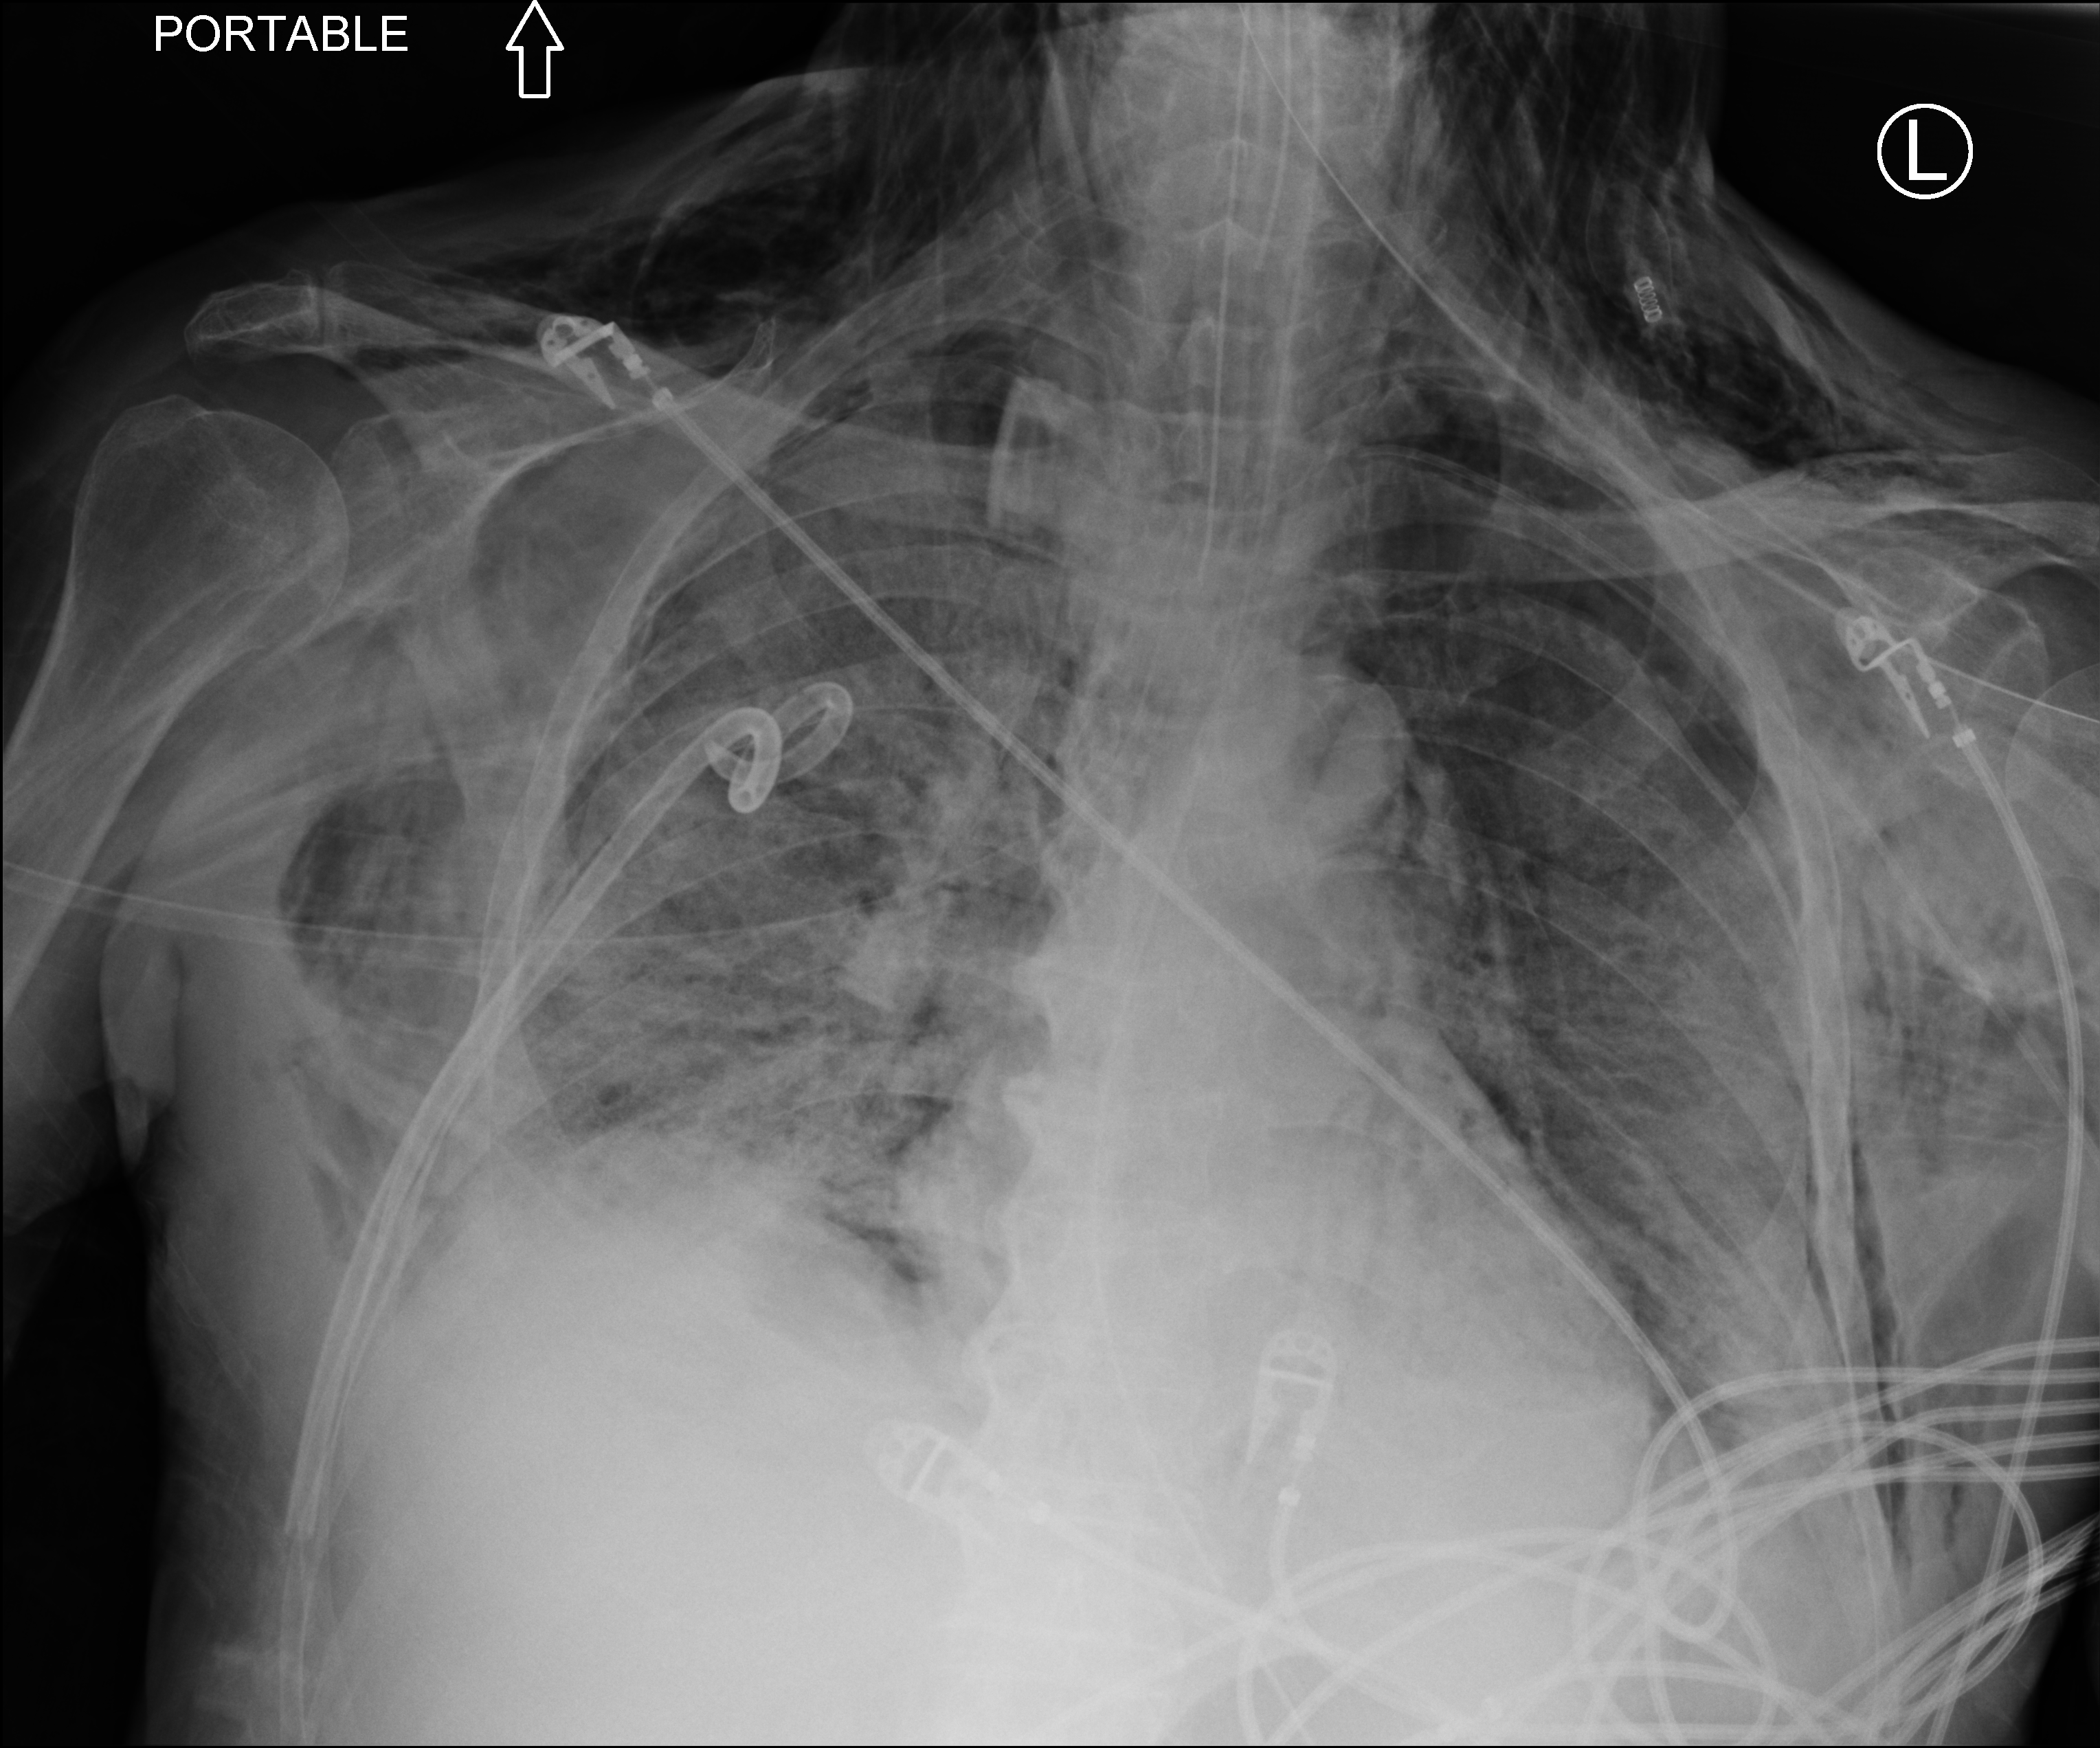
Chest X-ray (portable). Patient hospitalised with COVID-19; male, aged 75–90 years.
Admission-level facts for this patient (not findings on this image; timing relative to this image not recorded): COPD (admission record): no; admitted to intensive care during this hospital stay: yes; length of hospital stay: 30 days.